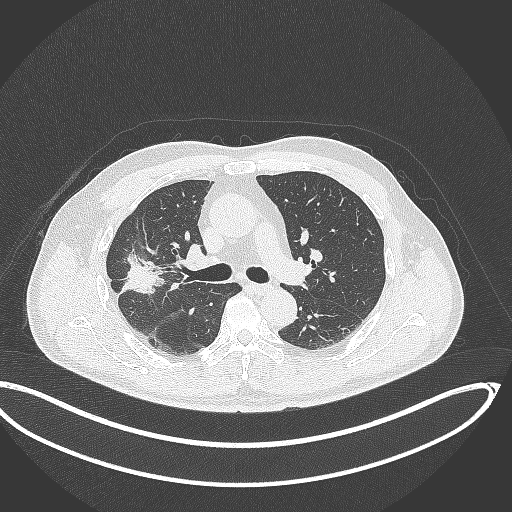
Chest CT, one axial slice. Position 214 of 391 along the scan axis. 120 kVp. Lung window (W 1500 / L -600 HU). 512 × 512 image matrix, field of view 439 × 439 mm. Male patient, age 63 years. Case-level facts recorded for this patient, not image findings: clinical TNM (as recorded): T1c N0 M0; histopathological grade: G2-3.
Structures marked on this image (rectangle marked by the reading radiologist):
- lung tumour (recorded histology: adenocarcinoma): bounding box (x1, y1, x2, y2) in pixels: (119, 248, 171, 302)